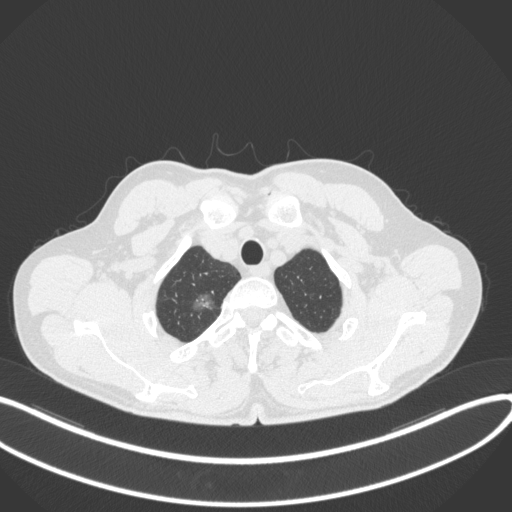
Chest CT, one axial slice; position 345 of 407 along the scan axis; reconstruction kernel B31f; lung window (W 1500 / L -600 HU); 1 mm slice thickness; 512 × 512 image matrix, field of view 400 × 400 mm. Patient: male, 58 years. Case-level facts recorded for this patient, not image findings: clinical TNM (as recorded): T1c N0 M0.
Structures marked on this image (bounding box drawn by a radiologist):
- lung tumour (recorded histology: adenocarcinoma): bounding box (x1, y1, x2, y2) in pixels: (183, 291, 215, 317)